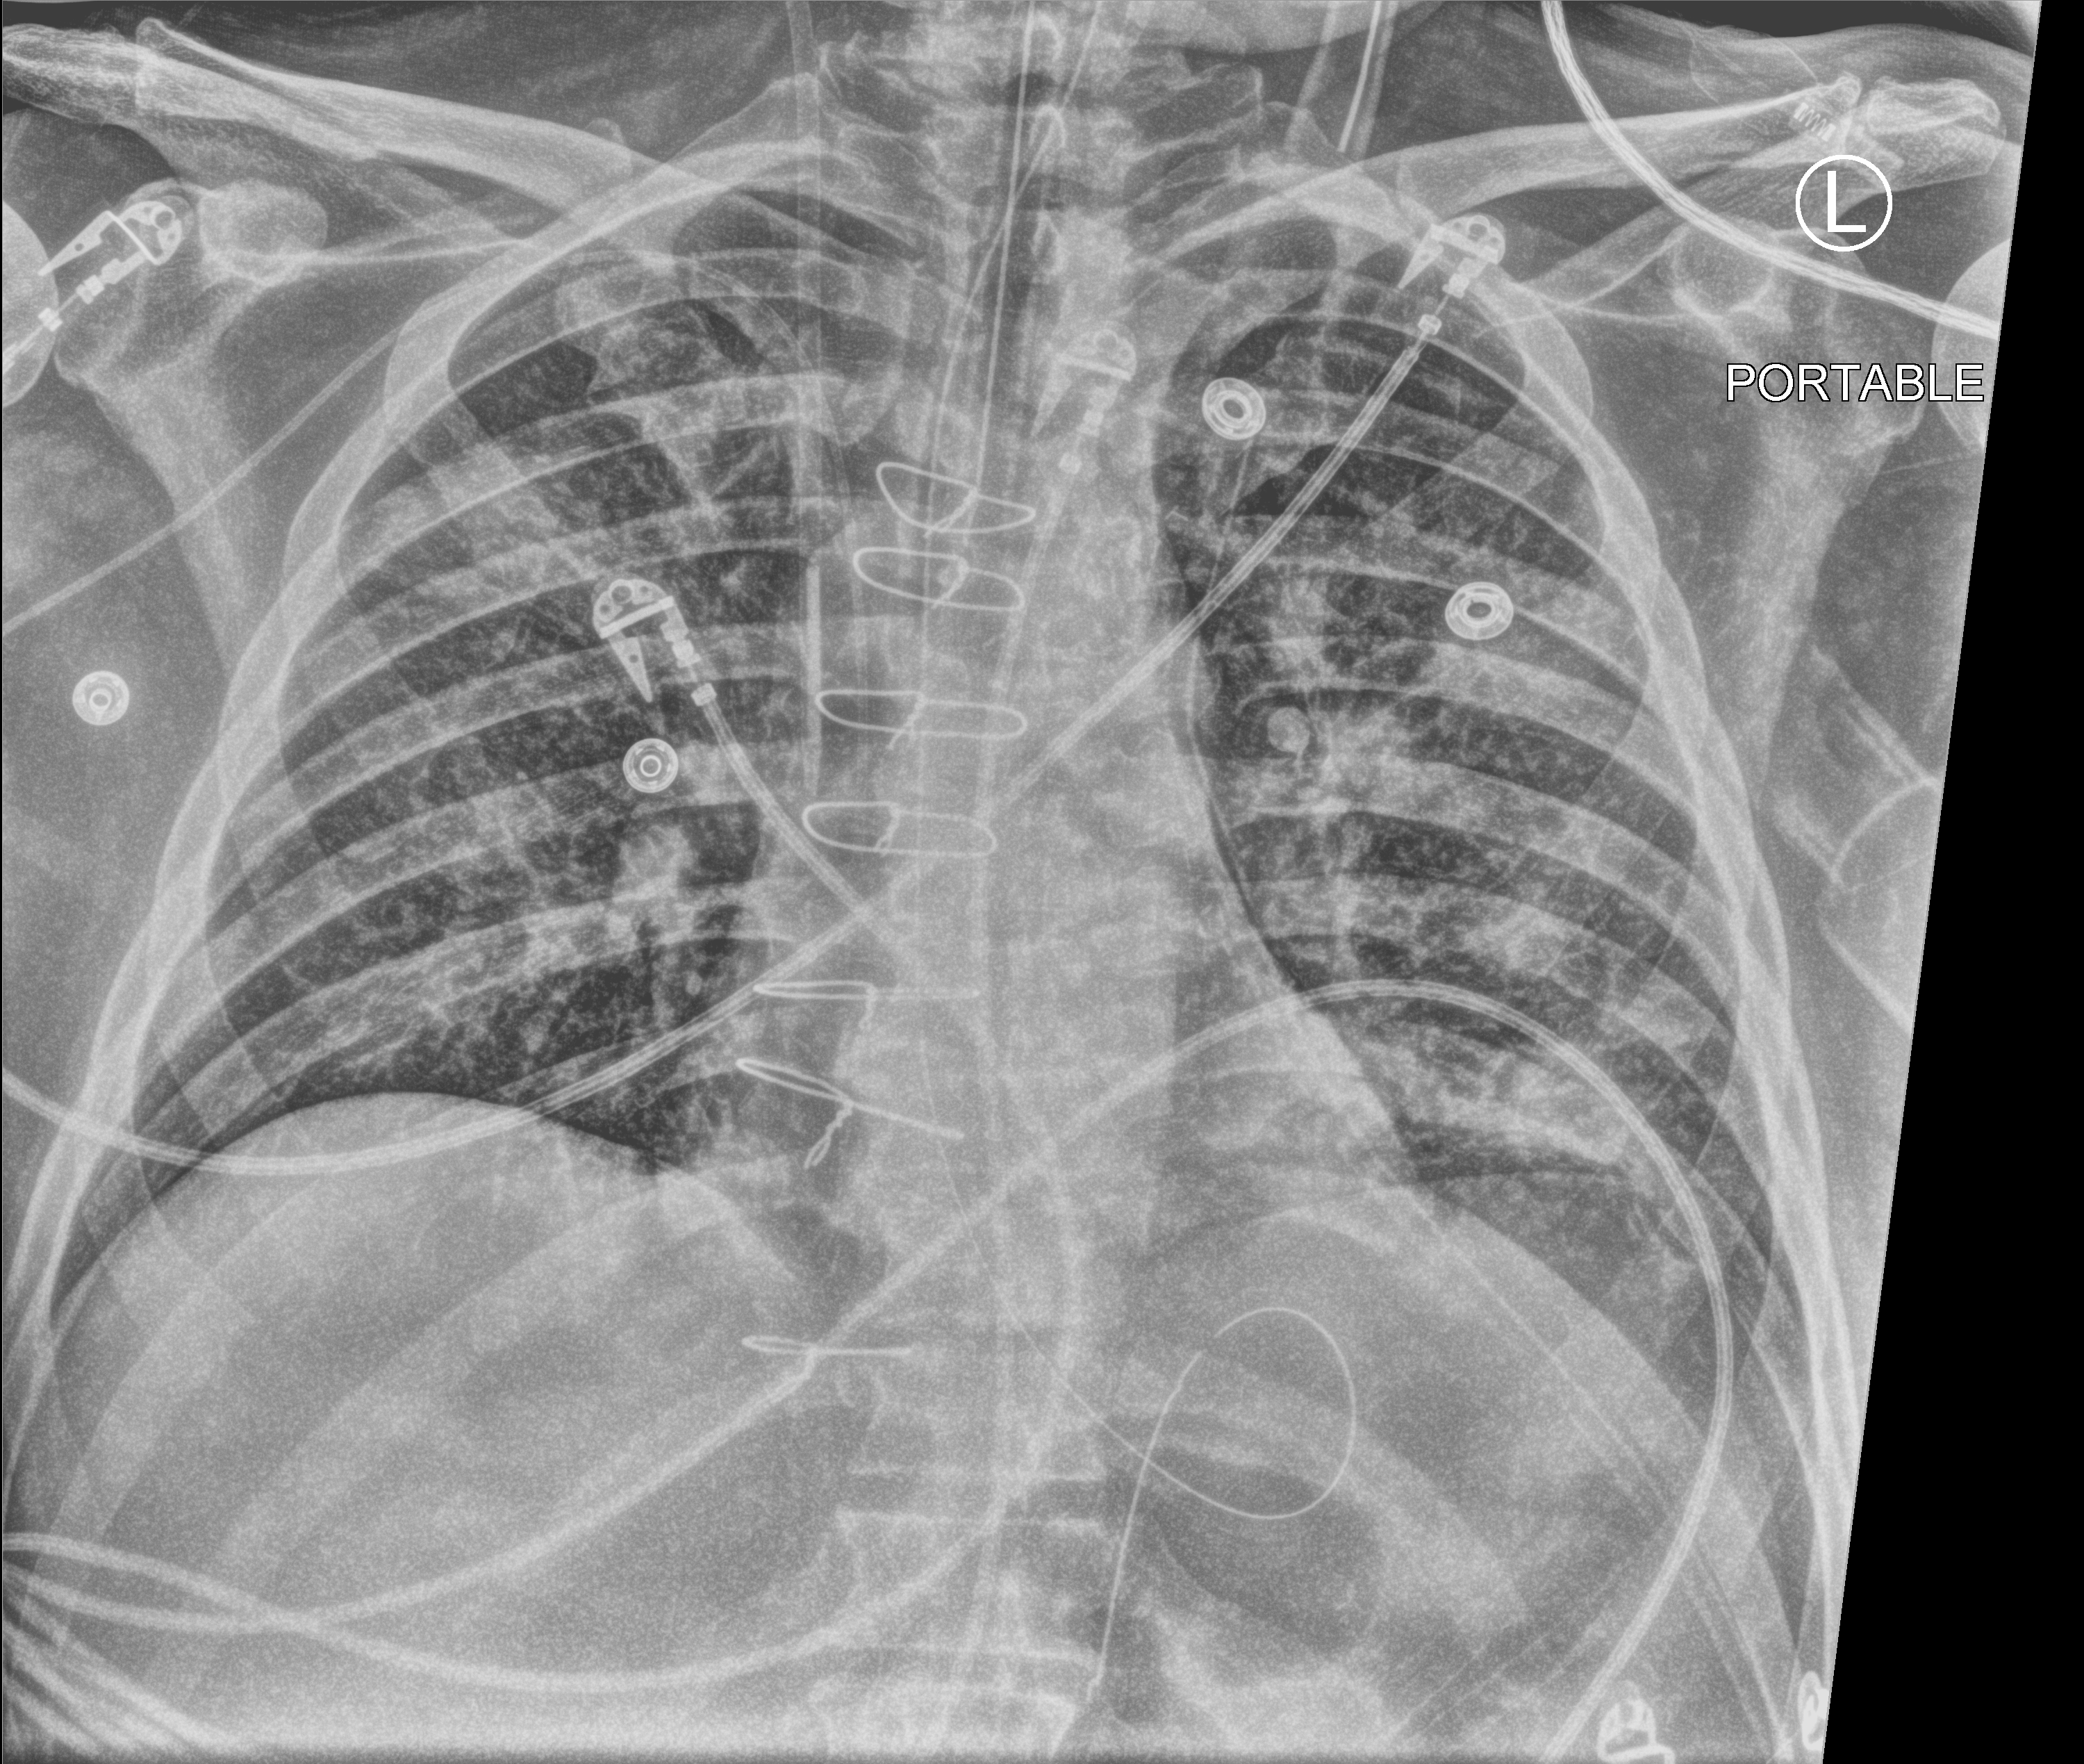
Portable chest radiograph, anteroposterior (AP) projection. Patient hospitalised with COVID-19; male, aged 60–74 years.
Hospital-stay facts (about this admission, not read from this image; timing relative to this image not recorded): admitted to intensive care during this hospital stay: yes.